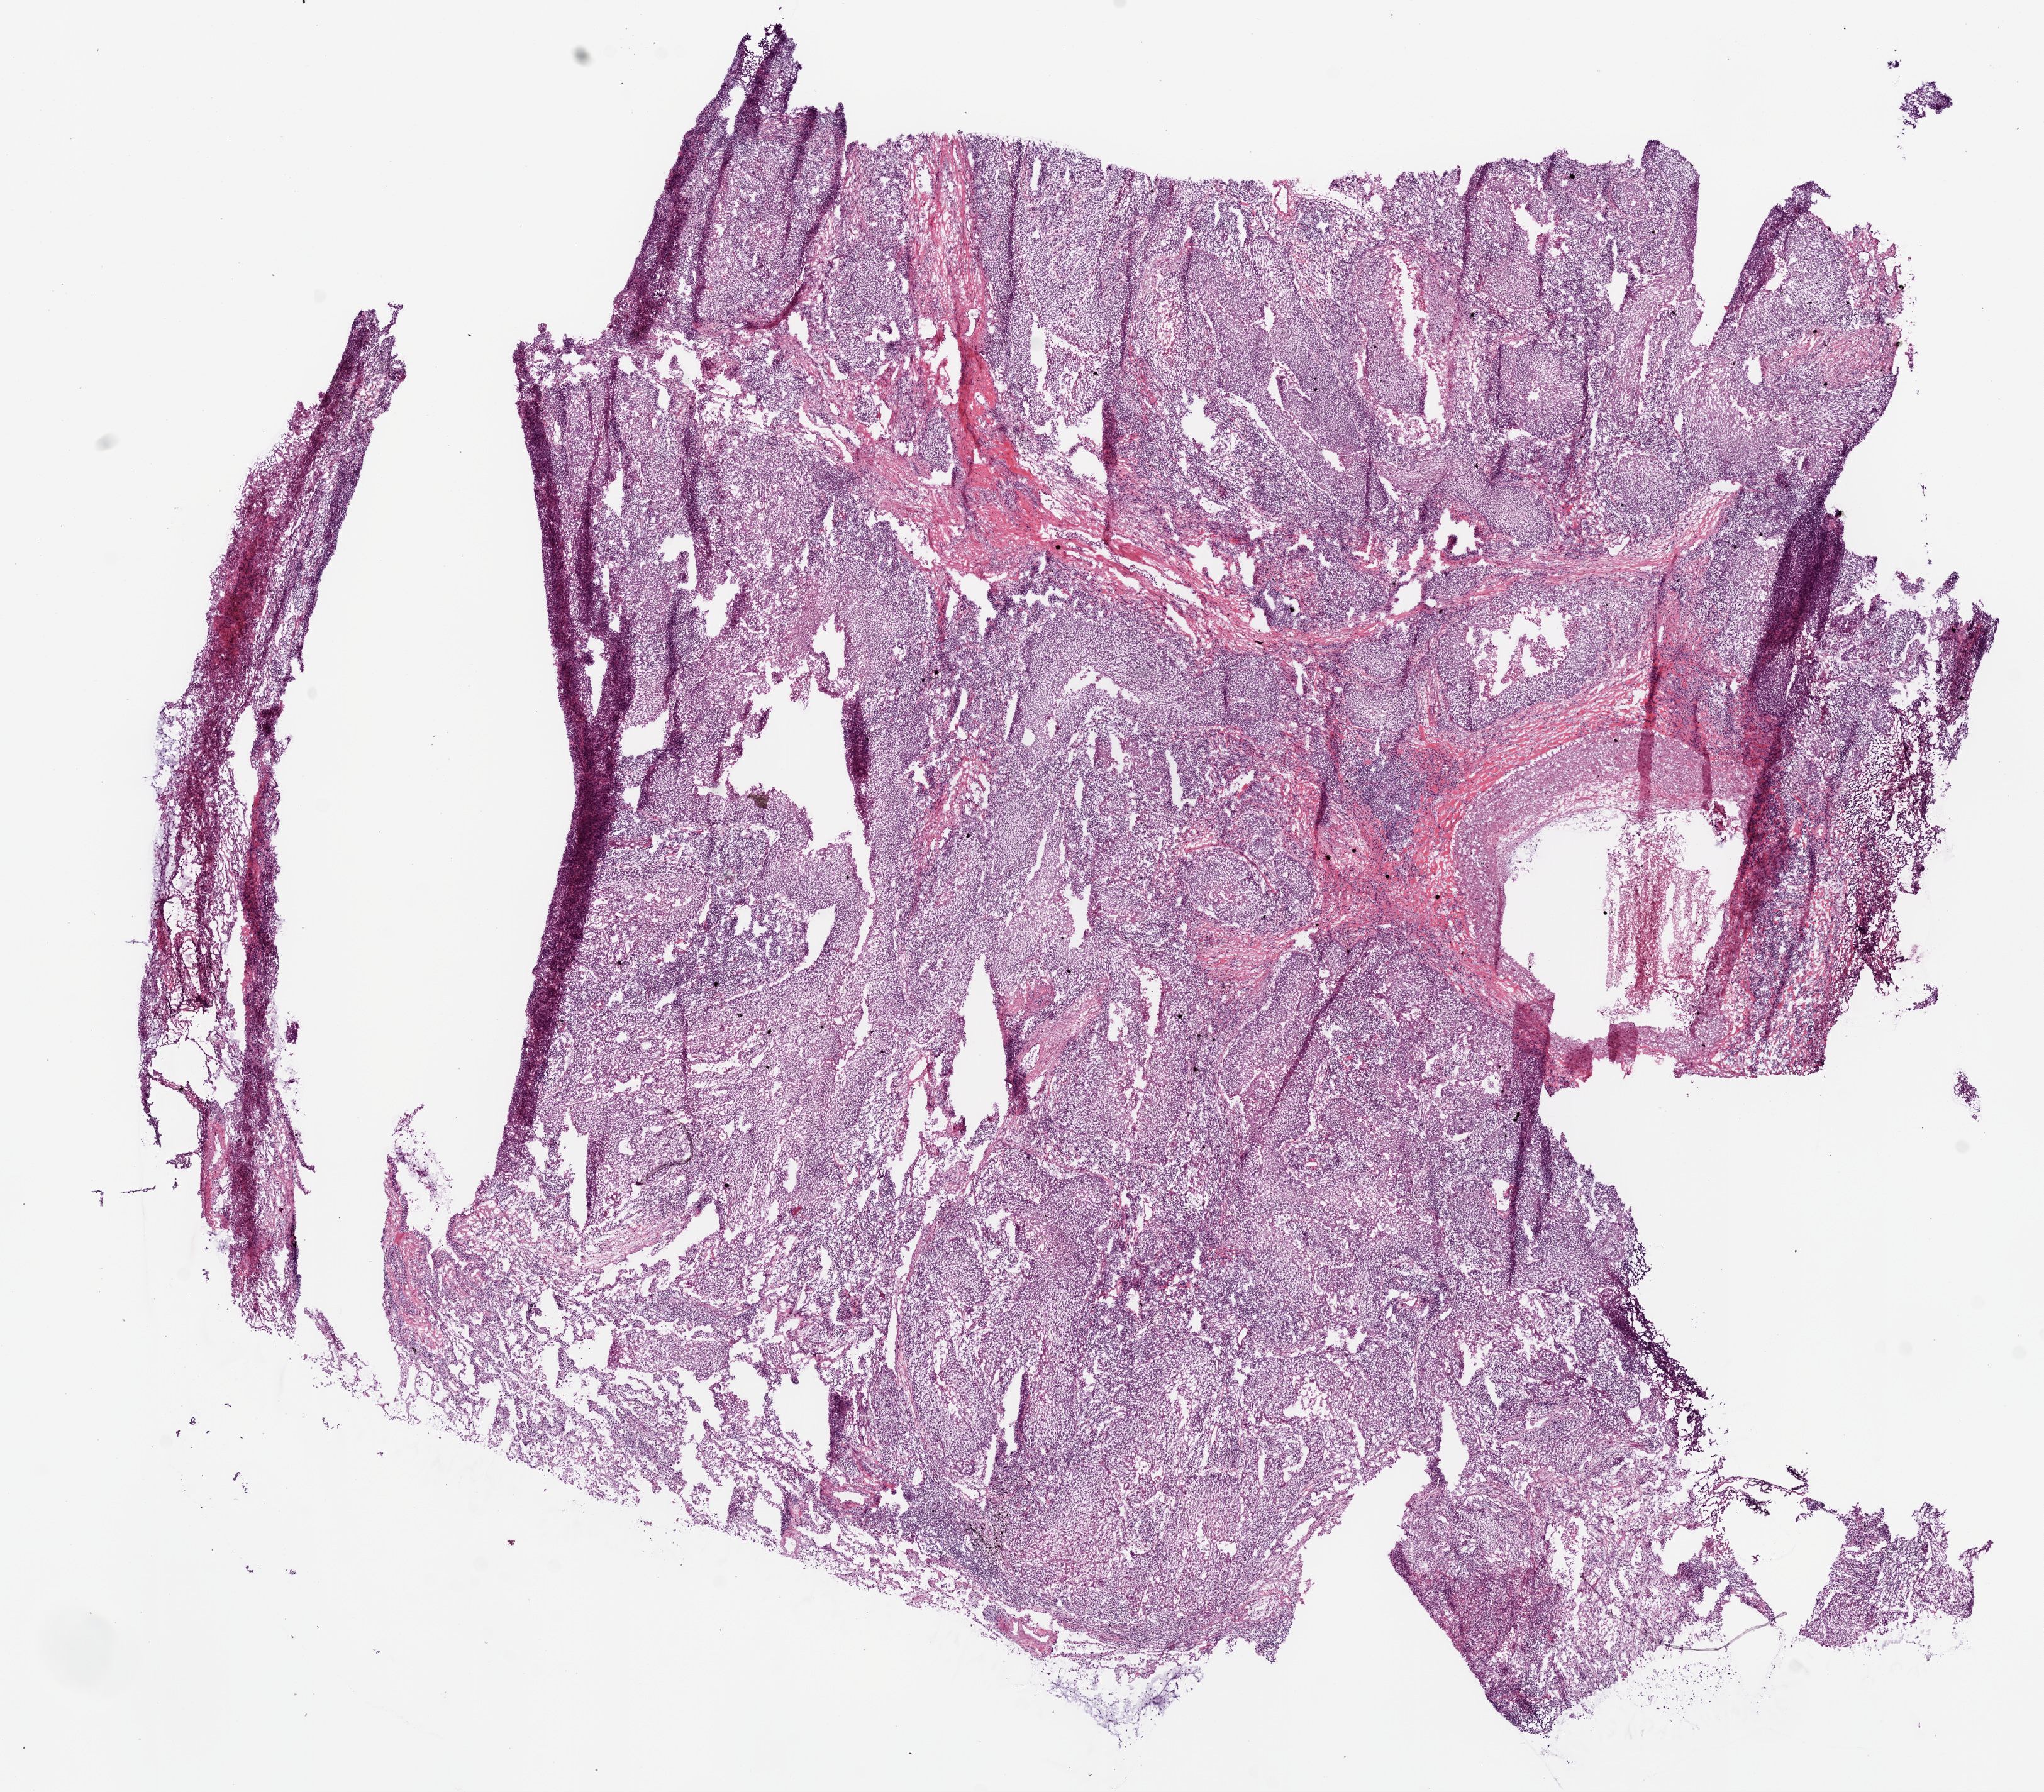
Whole-slide histology image, H&E — shown as a low-resolution overview of the whole scanned area (about 13.0 x 11.4 mm, from a 20x scan). Frozen section. Sample: primary tumour, lung. Female, age 75 years at initial diagnosis. Pathologist review of this section (percent, as recorded): tumour cells 84%, tumour nuclei 80%, normal cells 8%, stromal cells 5%, necrosis 3%.
Histologic diagnosis: Squamous cell carcinoma, NOS (upper lobe, lung). AJCC pathologic stage: IIA (6th edition).